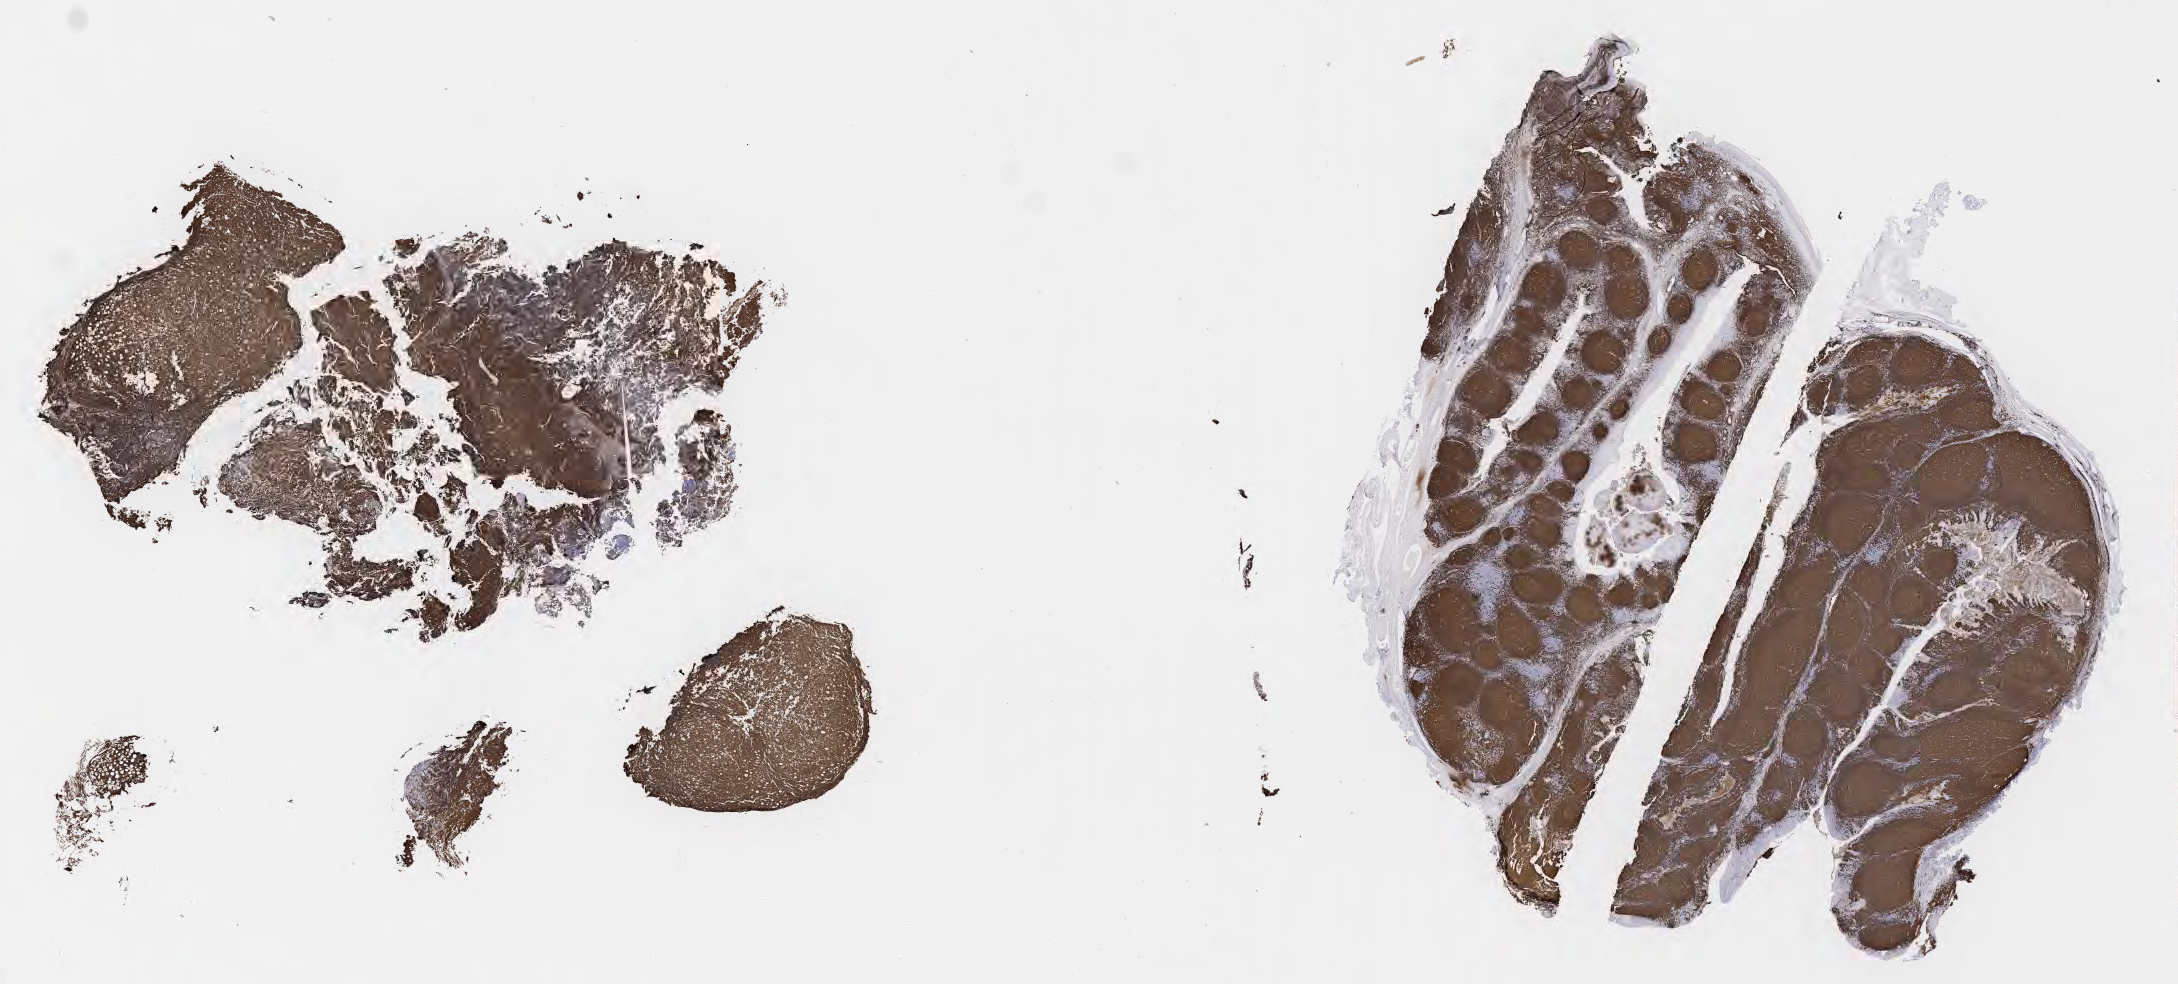
Whole-slide image, immunohistochemical stain for CD20, whole scanned area (about 35.2 x 15.9 mm) shown as a low-resolution overview, tumor tissue. Male patient, 23 years old.
• diagnosis: Burkitt lymphoma, NOS